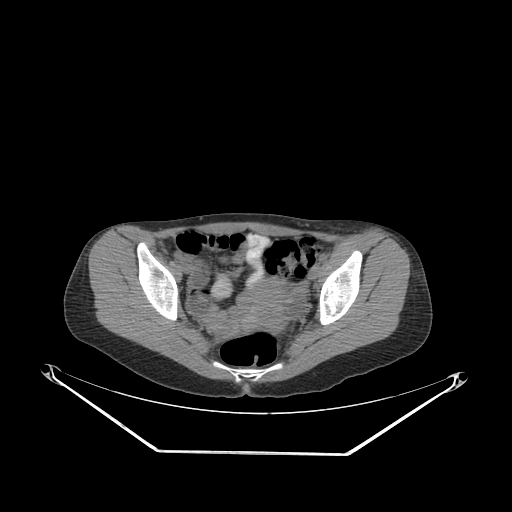
CT of an extremity soft-tissue mass (from a PET/CT study), one axial slice. Slice 81 of 267 in the series (ordered by position). 140 kVp. Soft-tissue window (W 400 / L 40 HU). 3.75 mm slice thickness. 512 × 512 image matrix, field of view 500 × 500 mm. Female patient. From the clinical record (not read from this slice): histological type: leiomyosarcoma; grade: high; site of the primary tumour: groin.
Outlined on this slice (expert contour drawn on MRI and transferred to this co-registered scan by the dataset authors):
- gross tumour volume including surrounding oedema: box from (x=331, y=240) to (x=375, y=252) px